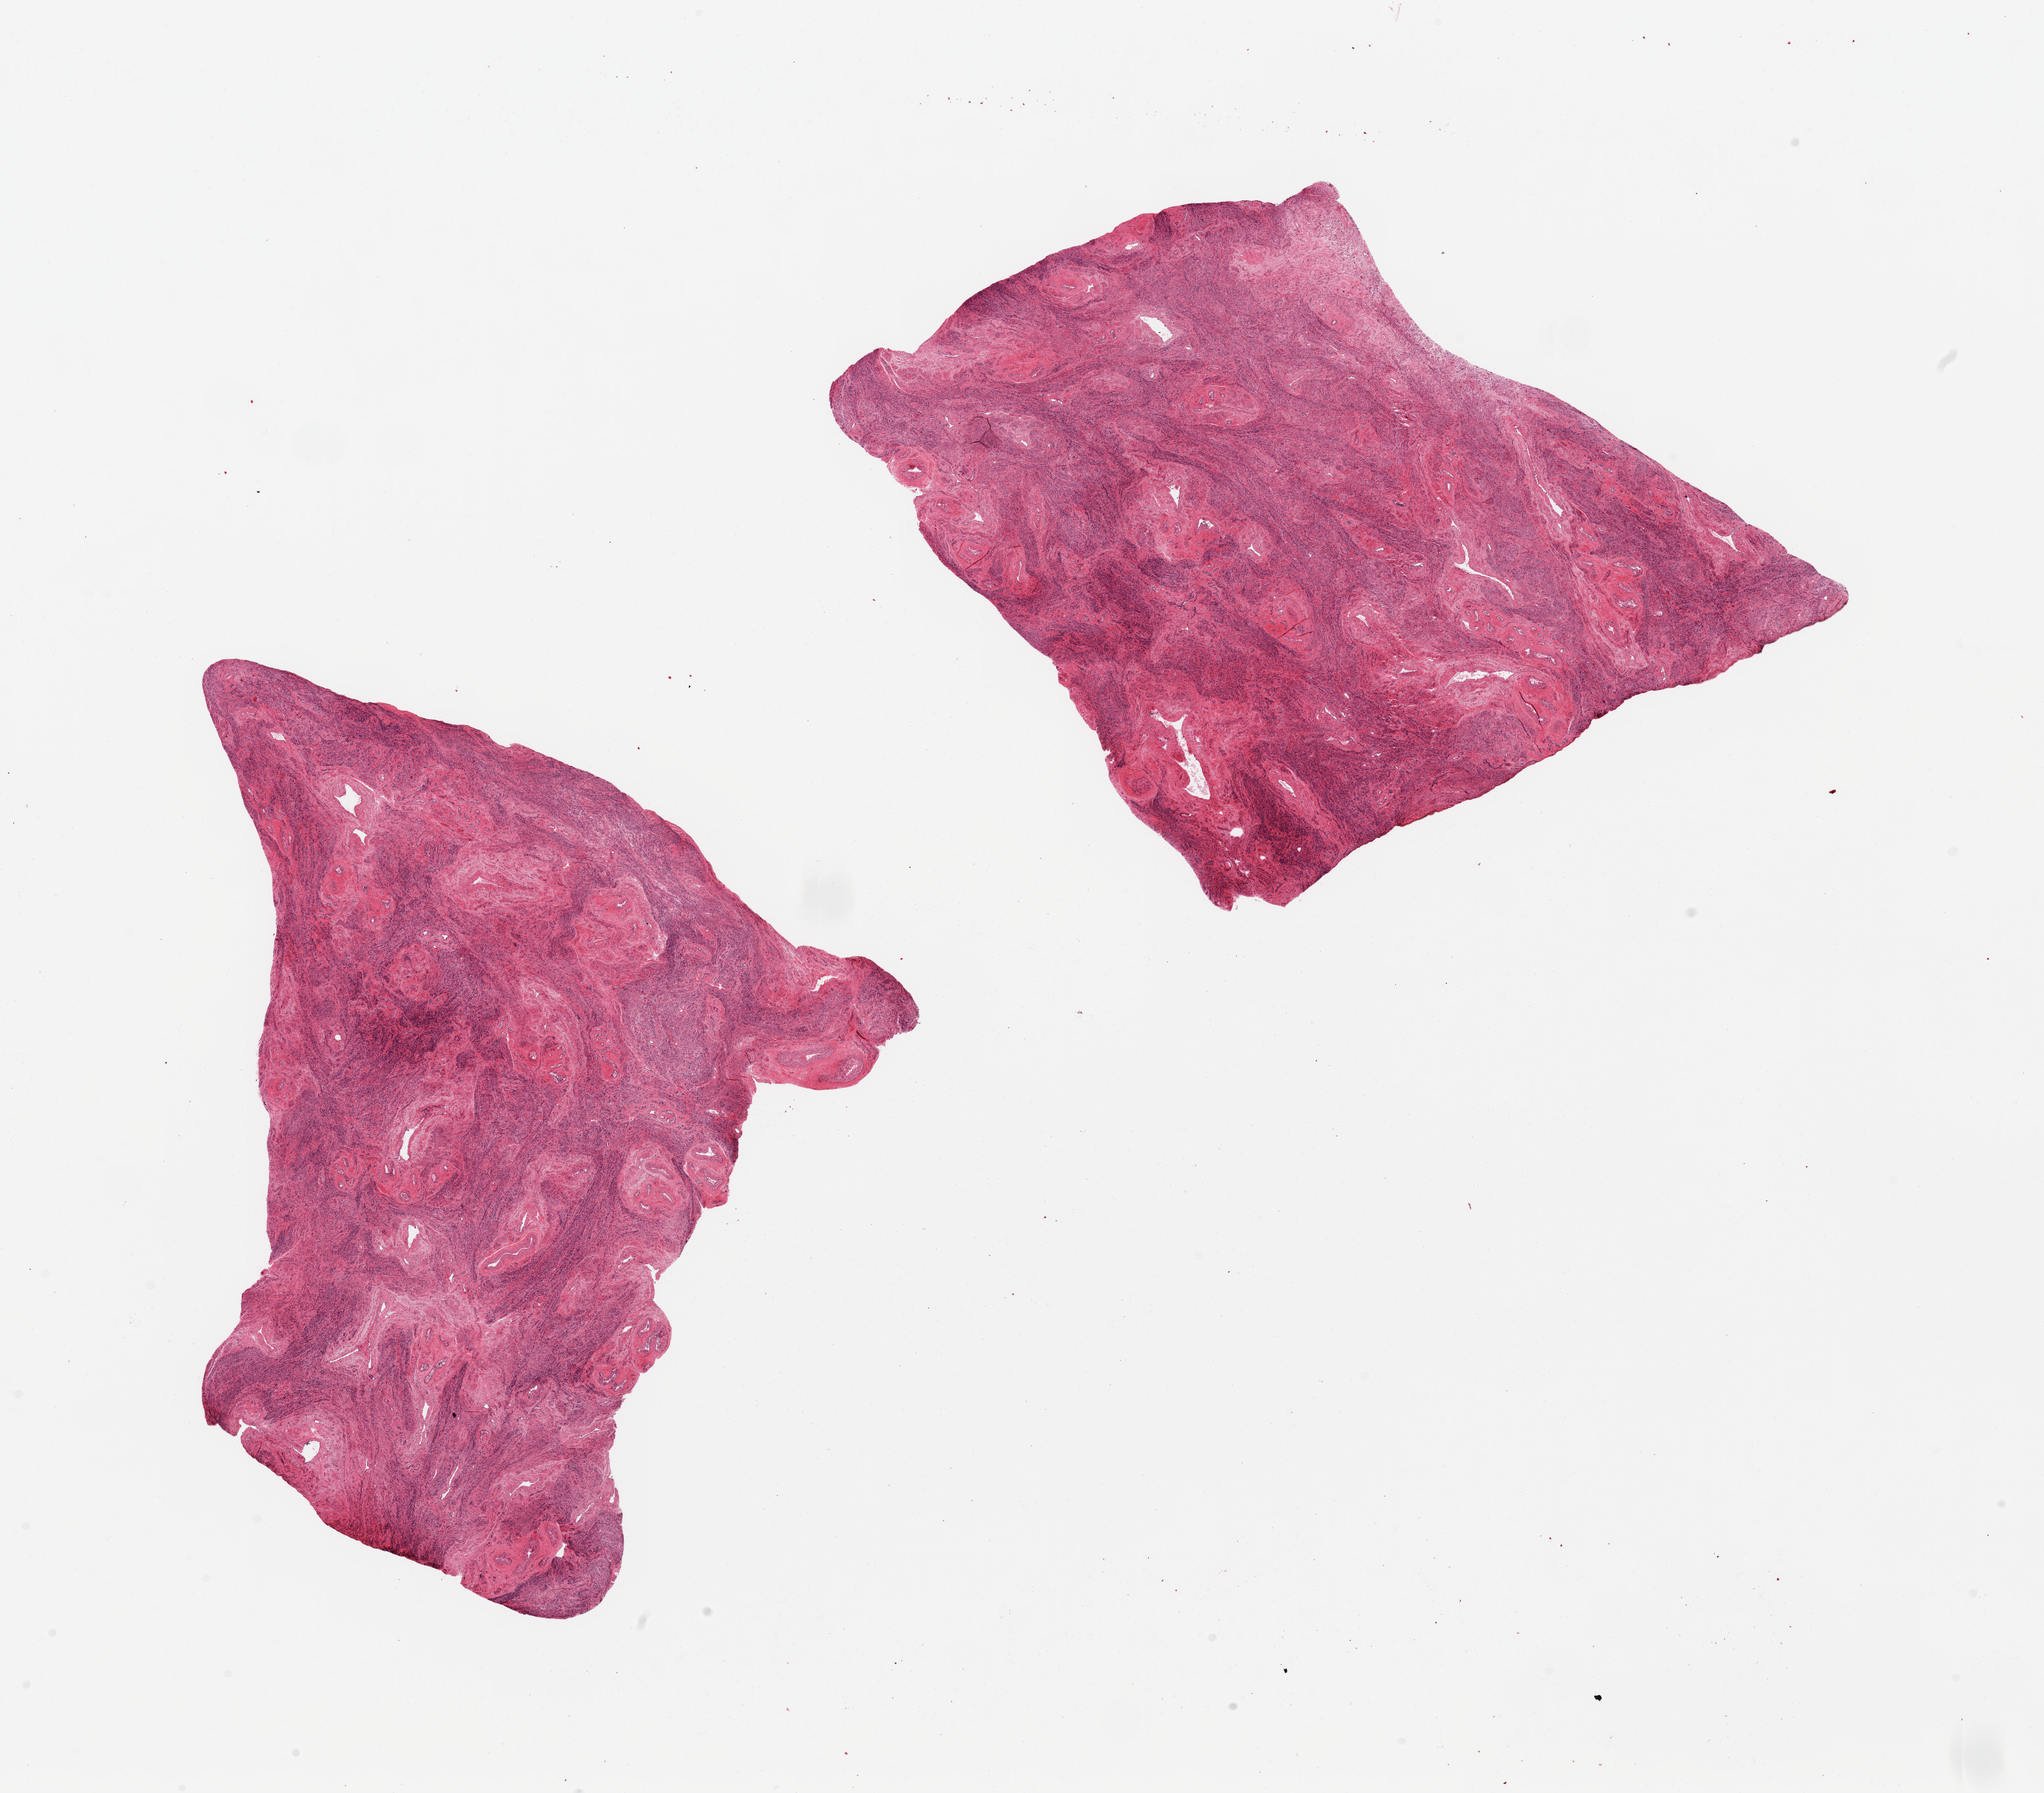
Haematoxylin and eosin whole-slide image, low-resolution overview of the scanned area, about 24.6 x 21.6 mm, PAXgene-fixed paraffin-embedded (PFPE) section, target tissue: uterus, tissue donor sample. Donor sex: female.
Pathologist's review note for this sample: 2 pieces, myometrium only.